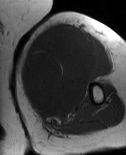
MRI of an extremity soft-tissue mass, one axial slice. MR volume resampled by the dataset authors to the PET/CT grid (not the native acquisition matrix). 3.27 mm slice thickness. 126 × 155 image matrix, field of view 123 × 151 mm. Female patient. Case-level facts recorded for this patient, not image findings: histological type: pleiomorphic leiomyosarcoma; grade: high; site of the primary tumour: left biceps.
Outlined on this slice (expert contour drawn on MRI and transferred to this co-registered scan by the dataset authors):
- gross tumour volume including surrounding oedema: box from (x=20, y=24) to (x=105, y=121) px
- gross tumour volume (mass): (x=20, y=24)–(x=98, y=116)